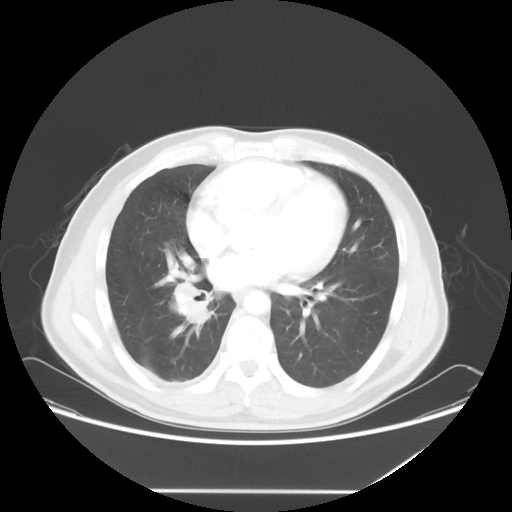
Chest CT, one axial slice; slice 26 of 60 in the series (ordered by position); reconstruction kernel STANDARD; lung window (W 1500 / L -600 HU); 5 mm slice thickness; 512 × 512 image matrix, field of view 419 × 419 mm. Male patient, age 48 years. From the clinical record (not read from this slice): clinical TNM (as recorded): T3 N3 M1a.
Annotated regions visible in this slice (bounding box drawn by a radiologist):
- lung tumour (recorded histology: squamous cell carcinoma): bounding box [x1, y1, x2, y2] px = [160, 273, 215, 333]